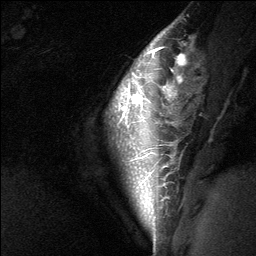
Breast MRI (dynamic contrast-enhanced), one sagittal slice. Position 51 of 64 along the scan axis. Dynamic contrast-enhanced study with each time point stored as its own series, time point 2 of 3 at this slice position (early post-contrast, ordered by acquisition time). 1.5 T. TE 4.8 ms, TR 27 ms. 256 × 256 image matrix, field of view 180 × 180 mm. Patient: female, 26 years. Case-level facts recorded for this patient, not image findings: setting: breast cancer imaged before/during neoadjuvant chemotherapy; receptor status: HR-positive, HER2-negative.
Structures marked on this image (semi-automatic segmentation, software-assisted and operator-edited):
- analysis volume of interest (the breast-tissue region the enhancement analysis was run in; not a lesion): bounding box (x1, y1, x2, y2) in pixels: (108, 43, 182, 138)
- tumour enhancement mask (voxels above the 90 % enhancement threshold inside the analysis volume of interest): (133, 47, 179, 102)